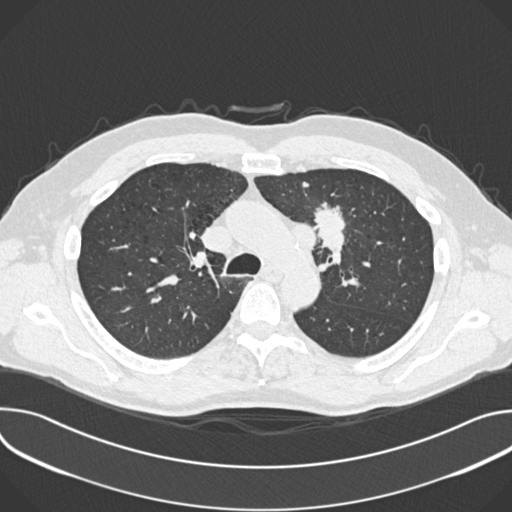
Low-dose screening chest CT, one axial slice; slice 261 of 361 in the series (ordered by position); 120 kVp; lung window (W 1500 / L -600 HU); 512 × 512 image matrix.
Structures marked on this image (manually delineated by an expert):
- lesion 1 (tumor, upper lobe of left lung): bounding box (x1, y1, x2, y2) in pixels: (315, 207, 346, 248)